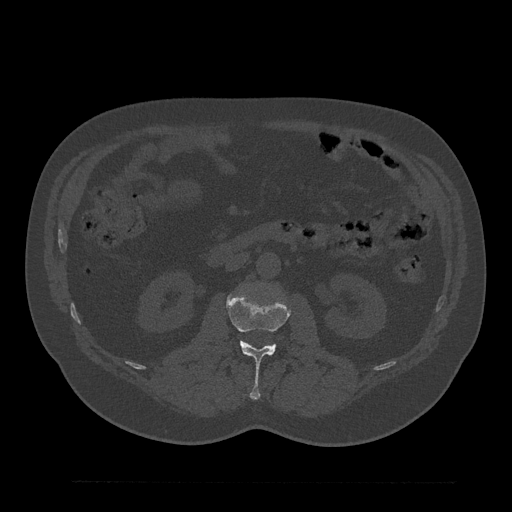
CT including the spine, one axial slice. Reconstruction kernel Br40s/3. 120 kVp. Bone window (W 1800 / L 400 HU). 512 × 512 image matrix, field of view 430 × 430 mm. Male patient, age 61 years. Case-level facts recorded for this patient, not image findings: primary cancer: prostate.
Annotated regions visible in this slice (semi-automatic segmentation, software-assisted and operator-edited):
- L2 vertebra: bounding box (x1, y1, x2, y2) in pixels: (227, 289, 291, 400)